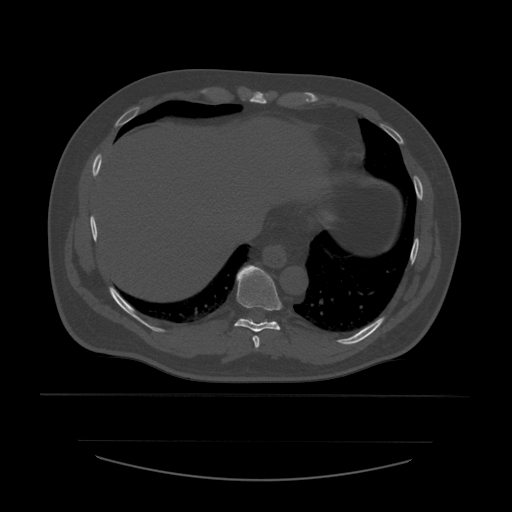
CT including the spine, one axial slice; slice 316 of 532 in the series (ordered by position); reconstruction kernel STANDARD; bone window (W 1800 / L 400 HU); 1.25 mm slice thickness; 512 × 512 image matrix, field of view 441 × 441 mm. Patient age 44 years. From the clinical record (not read from this slice): primary cancer: soft tissue sarcoma.
Outlined on this slice (semi-automatically segmented with operator editing):
- T8 vertebra: bounding box <253,336,260,349> (left, top, right, bottom; pixels)
- T9 vertebra: <235,266,283,332>